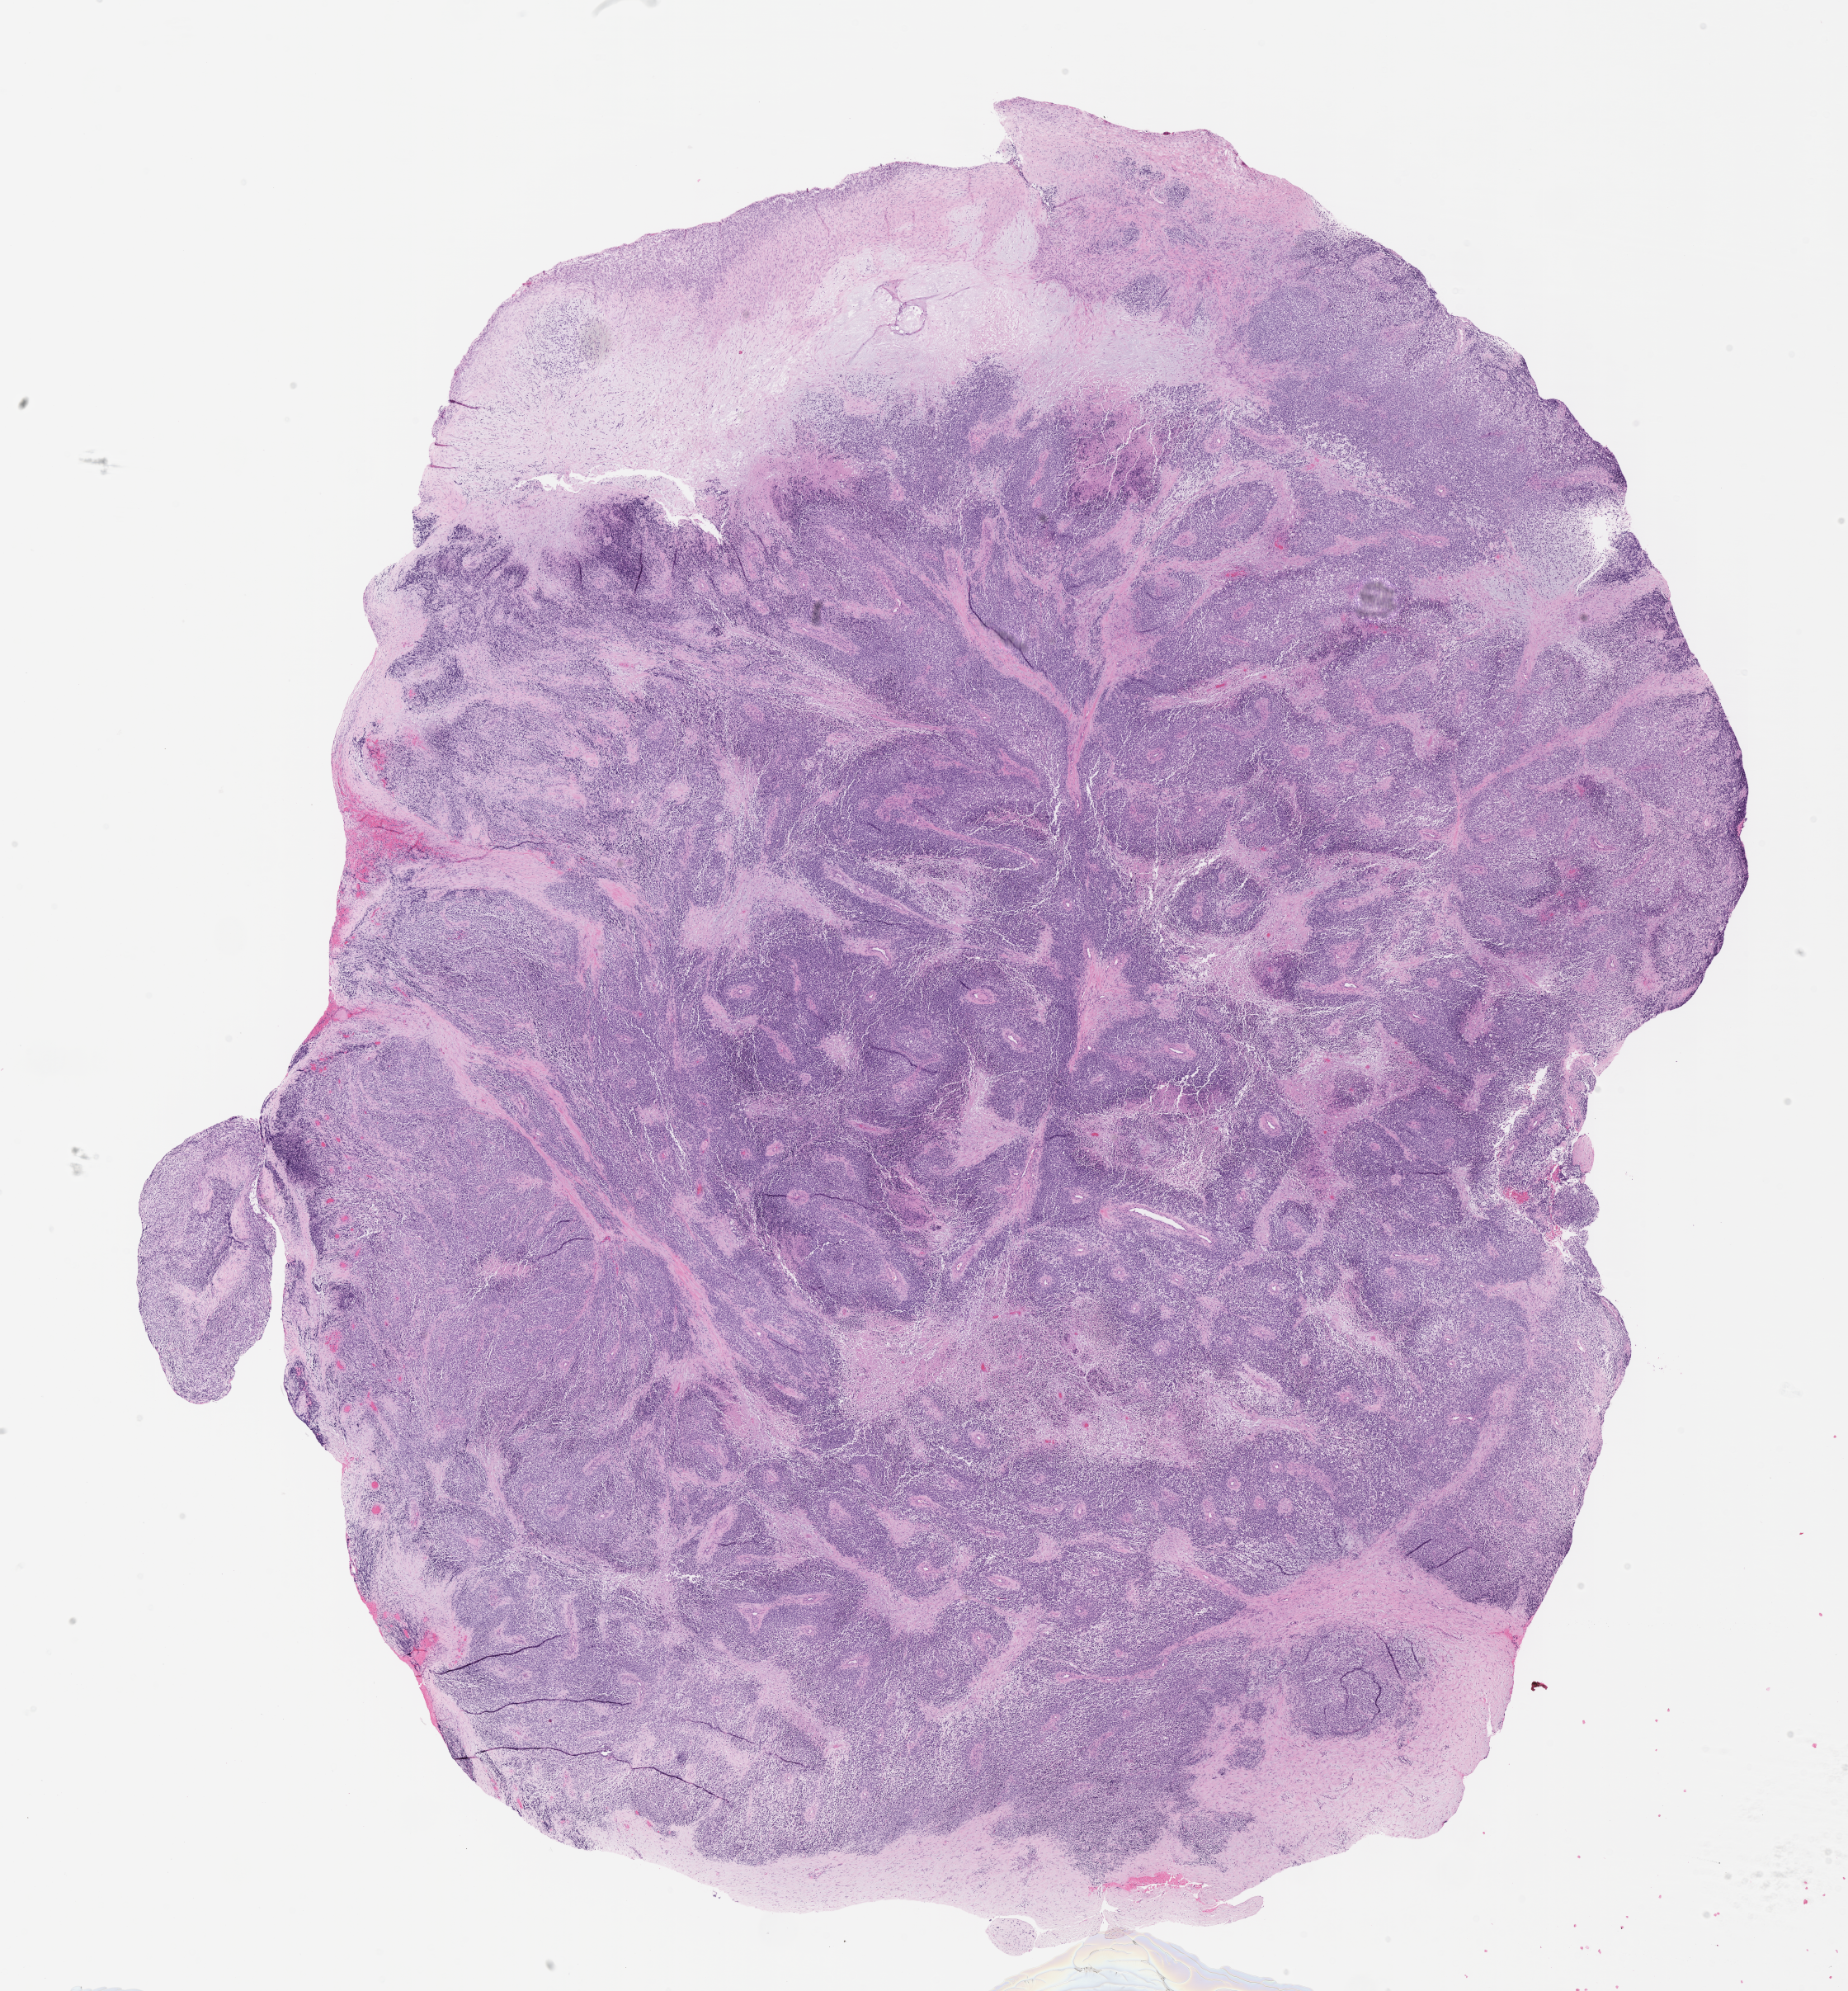
Whole-slide image, H&E stain of tumor tissue — a low-resolution overview of the entire scanned area, about 18.1 x 19.5 mm, FFPE section, site: peritoneum. Female patient, age at diagnosis 5.4 years.
Metastatic status at presentation (as recorded): metastatic (confirmed). Diagnosis: rhabdomyosarcoma; histological classification: embryonal rhabdomyosarcoma. Stage (as recorded): 4.